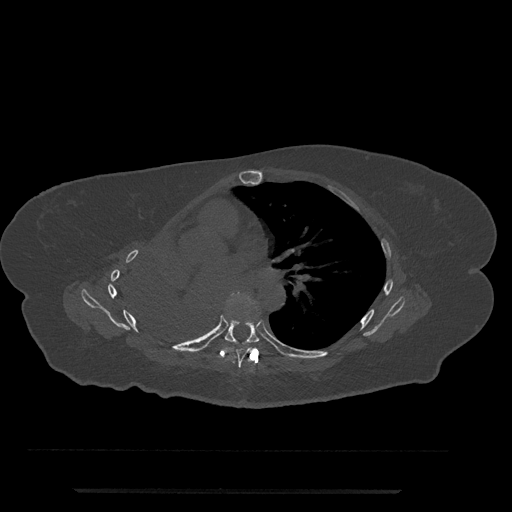
CT including the spine, one axial slice; slice 468 of 797 in the series (ordered by position); reconstruction kernel Br40s/3; bone window (W 1800 / L 400 HU); 0.5 mm slice thickness; 512 × 512 image matrix. Patient: female, 51 years. From the clinical record (not read from this slice): primary cancer: neuro; vertebrae with lytic lesions (as recorded): T8.
Structures marked on this image (semi-automatic segmentation, software-assisted and operator-edited):
- T6 vertebra: bounding box [x1, y1, x2, y2] px = [223, 322, 253, 368]
- T7 vertebra: [225, 317, 260, 345]